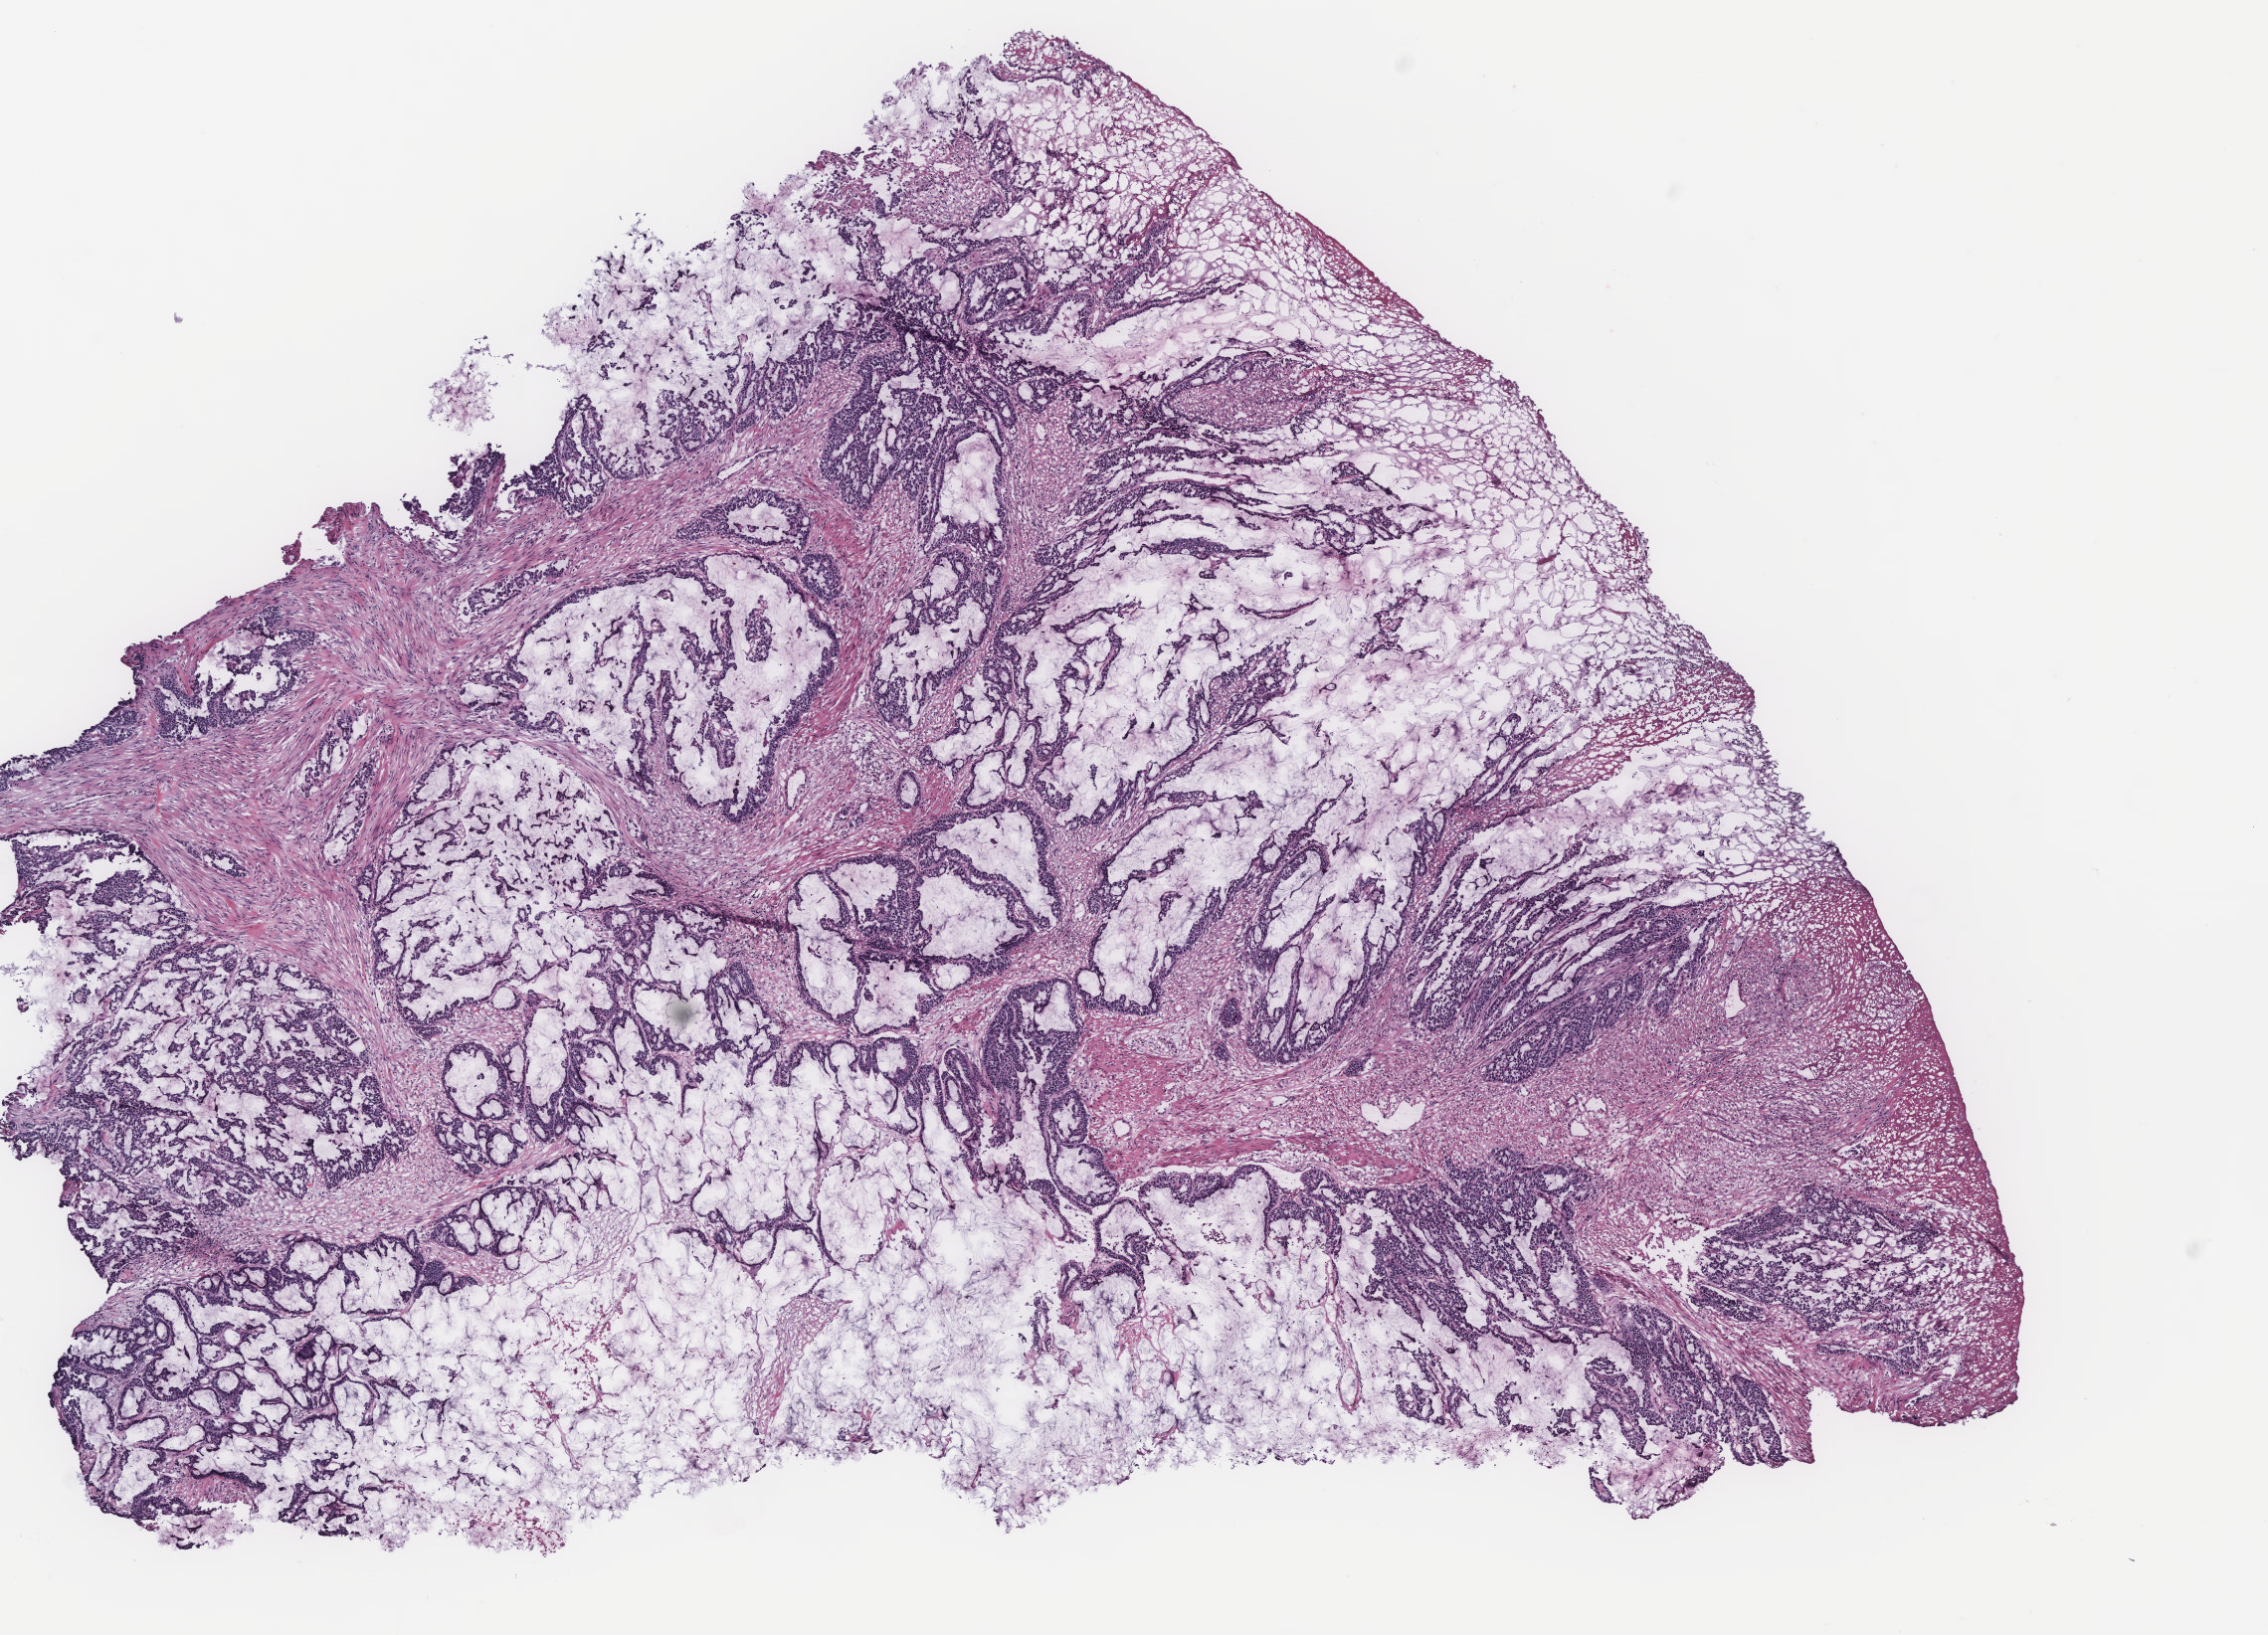
H&E-stained whole-slide image — shown as a low-resolution overview of the whole scanned area (about 9.1 x 6.6 mm, acquisition: 40x scan); colon, tissue type not recorded.
Patient diagnosis (cohort enrolment): colon cancer (colon).